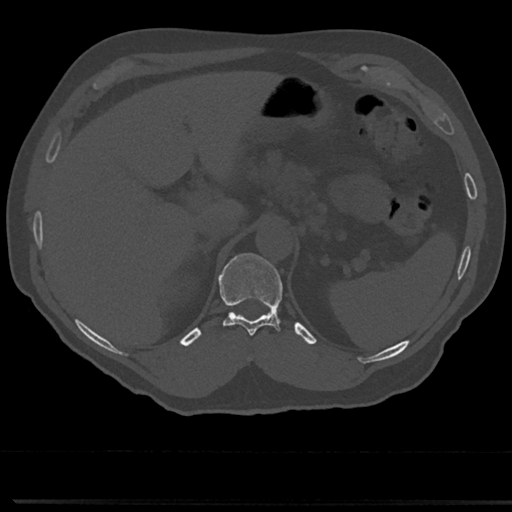
CT including the spine, one axial slice; reconstruction kernel Br40s/3; 120 kVp; bone window (W 1800 / L 400 HU); 0.5 mm slice thickness; 512 × 512 image matrix, field of view 355 × 355 mm. Male patient, age 61 years. Case-level facts recorded for this patient, not image findings: primary cancer: prostate.
Annotated regions visible in this slice (semi-automatically segmented with operator editing):
- T11 vertebra: bounding box <219,253,283,336> (left, top, right, bottom; pixels)